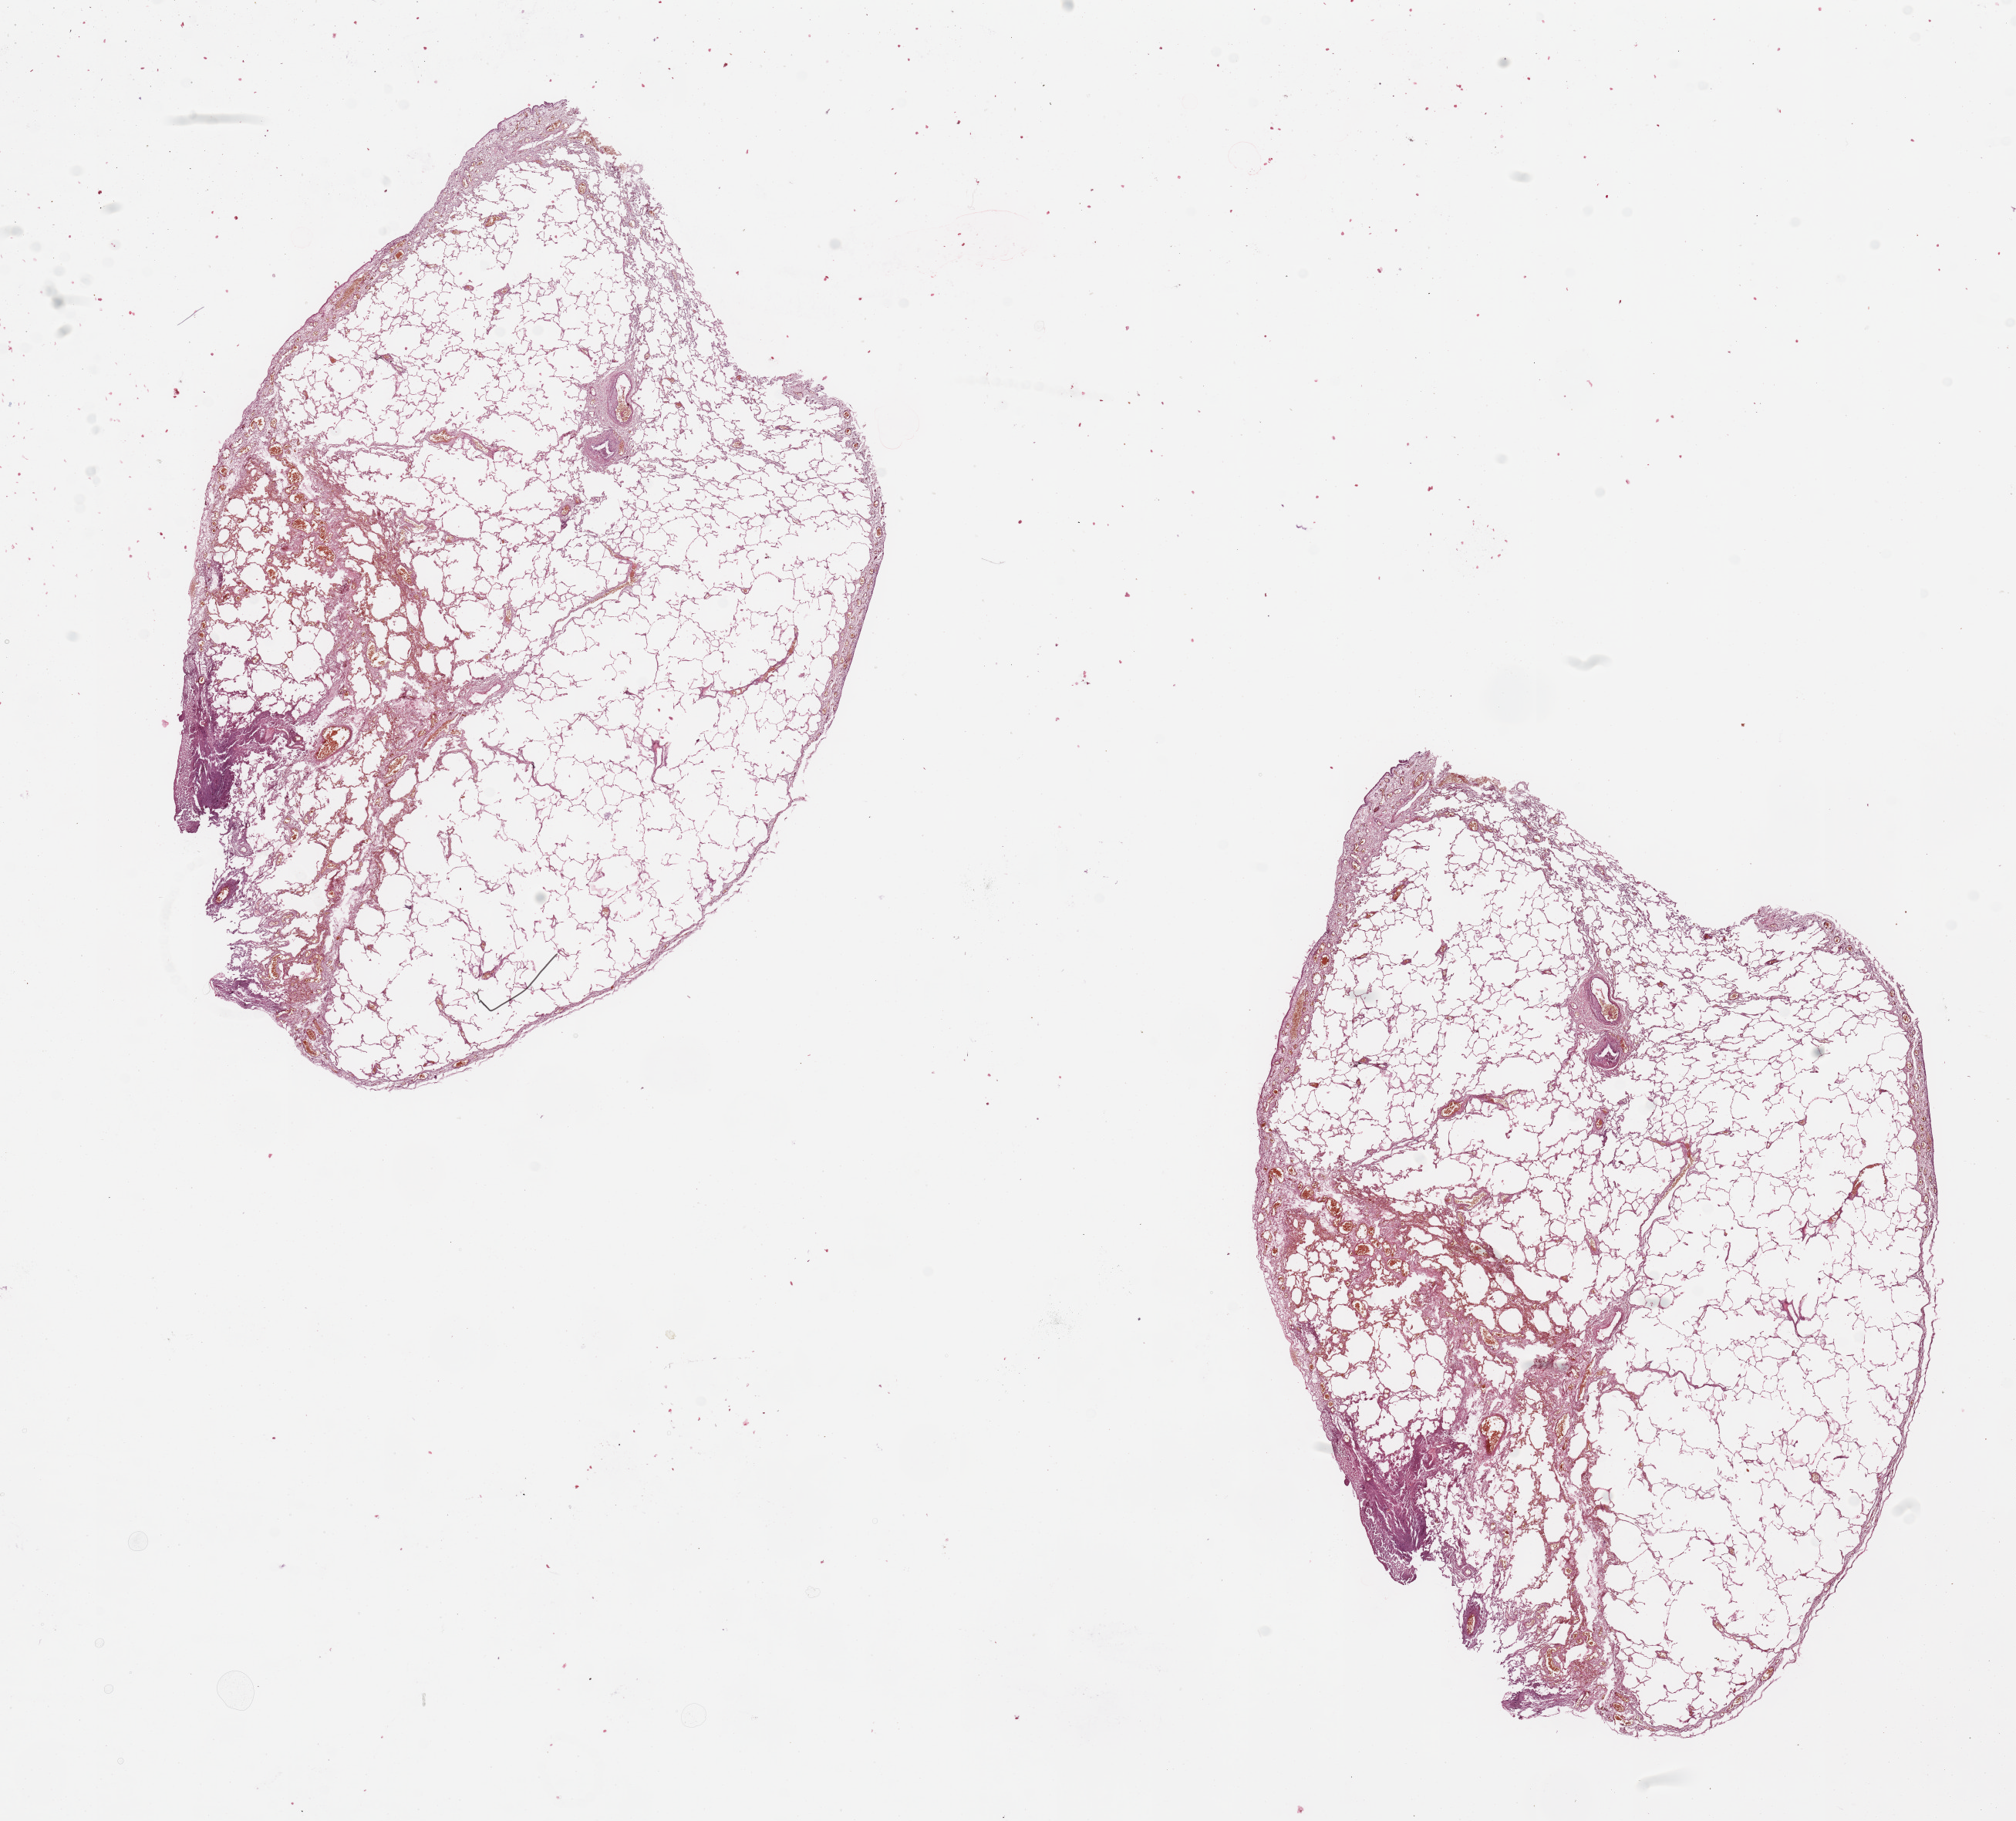
Digitized Hematoxylin and eosin (H&E) stained tissue section (whole slide), low-resolution overview of the scanned area, about 20.7 x 18.7 mm (slide scanned at 20x). Normal (non-tumour) tissue sample, sampled site: lung. 56-year-old male patient.
This section: normal (non-tumour) tissue from the same patient. Patient diagnosis: Adenocarcinoma, NOS.